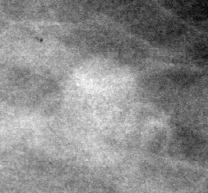
Crop from a digitized film mammogram around one marked abnormality; left breast; MLO view; BI-RADS breast density category 1 (scale 1–4).
Marked abnormality: mass, shape lymph node, margins circumscribed; BI-RADS assessment category 3; subtlety rating 2 on a 1 (subtle) to 5 (obvious) scale; benign without callback (not worked up further).